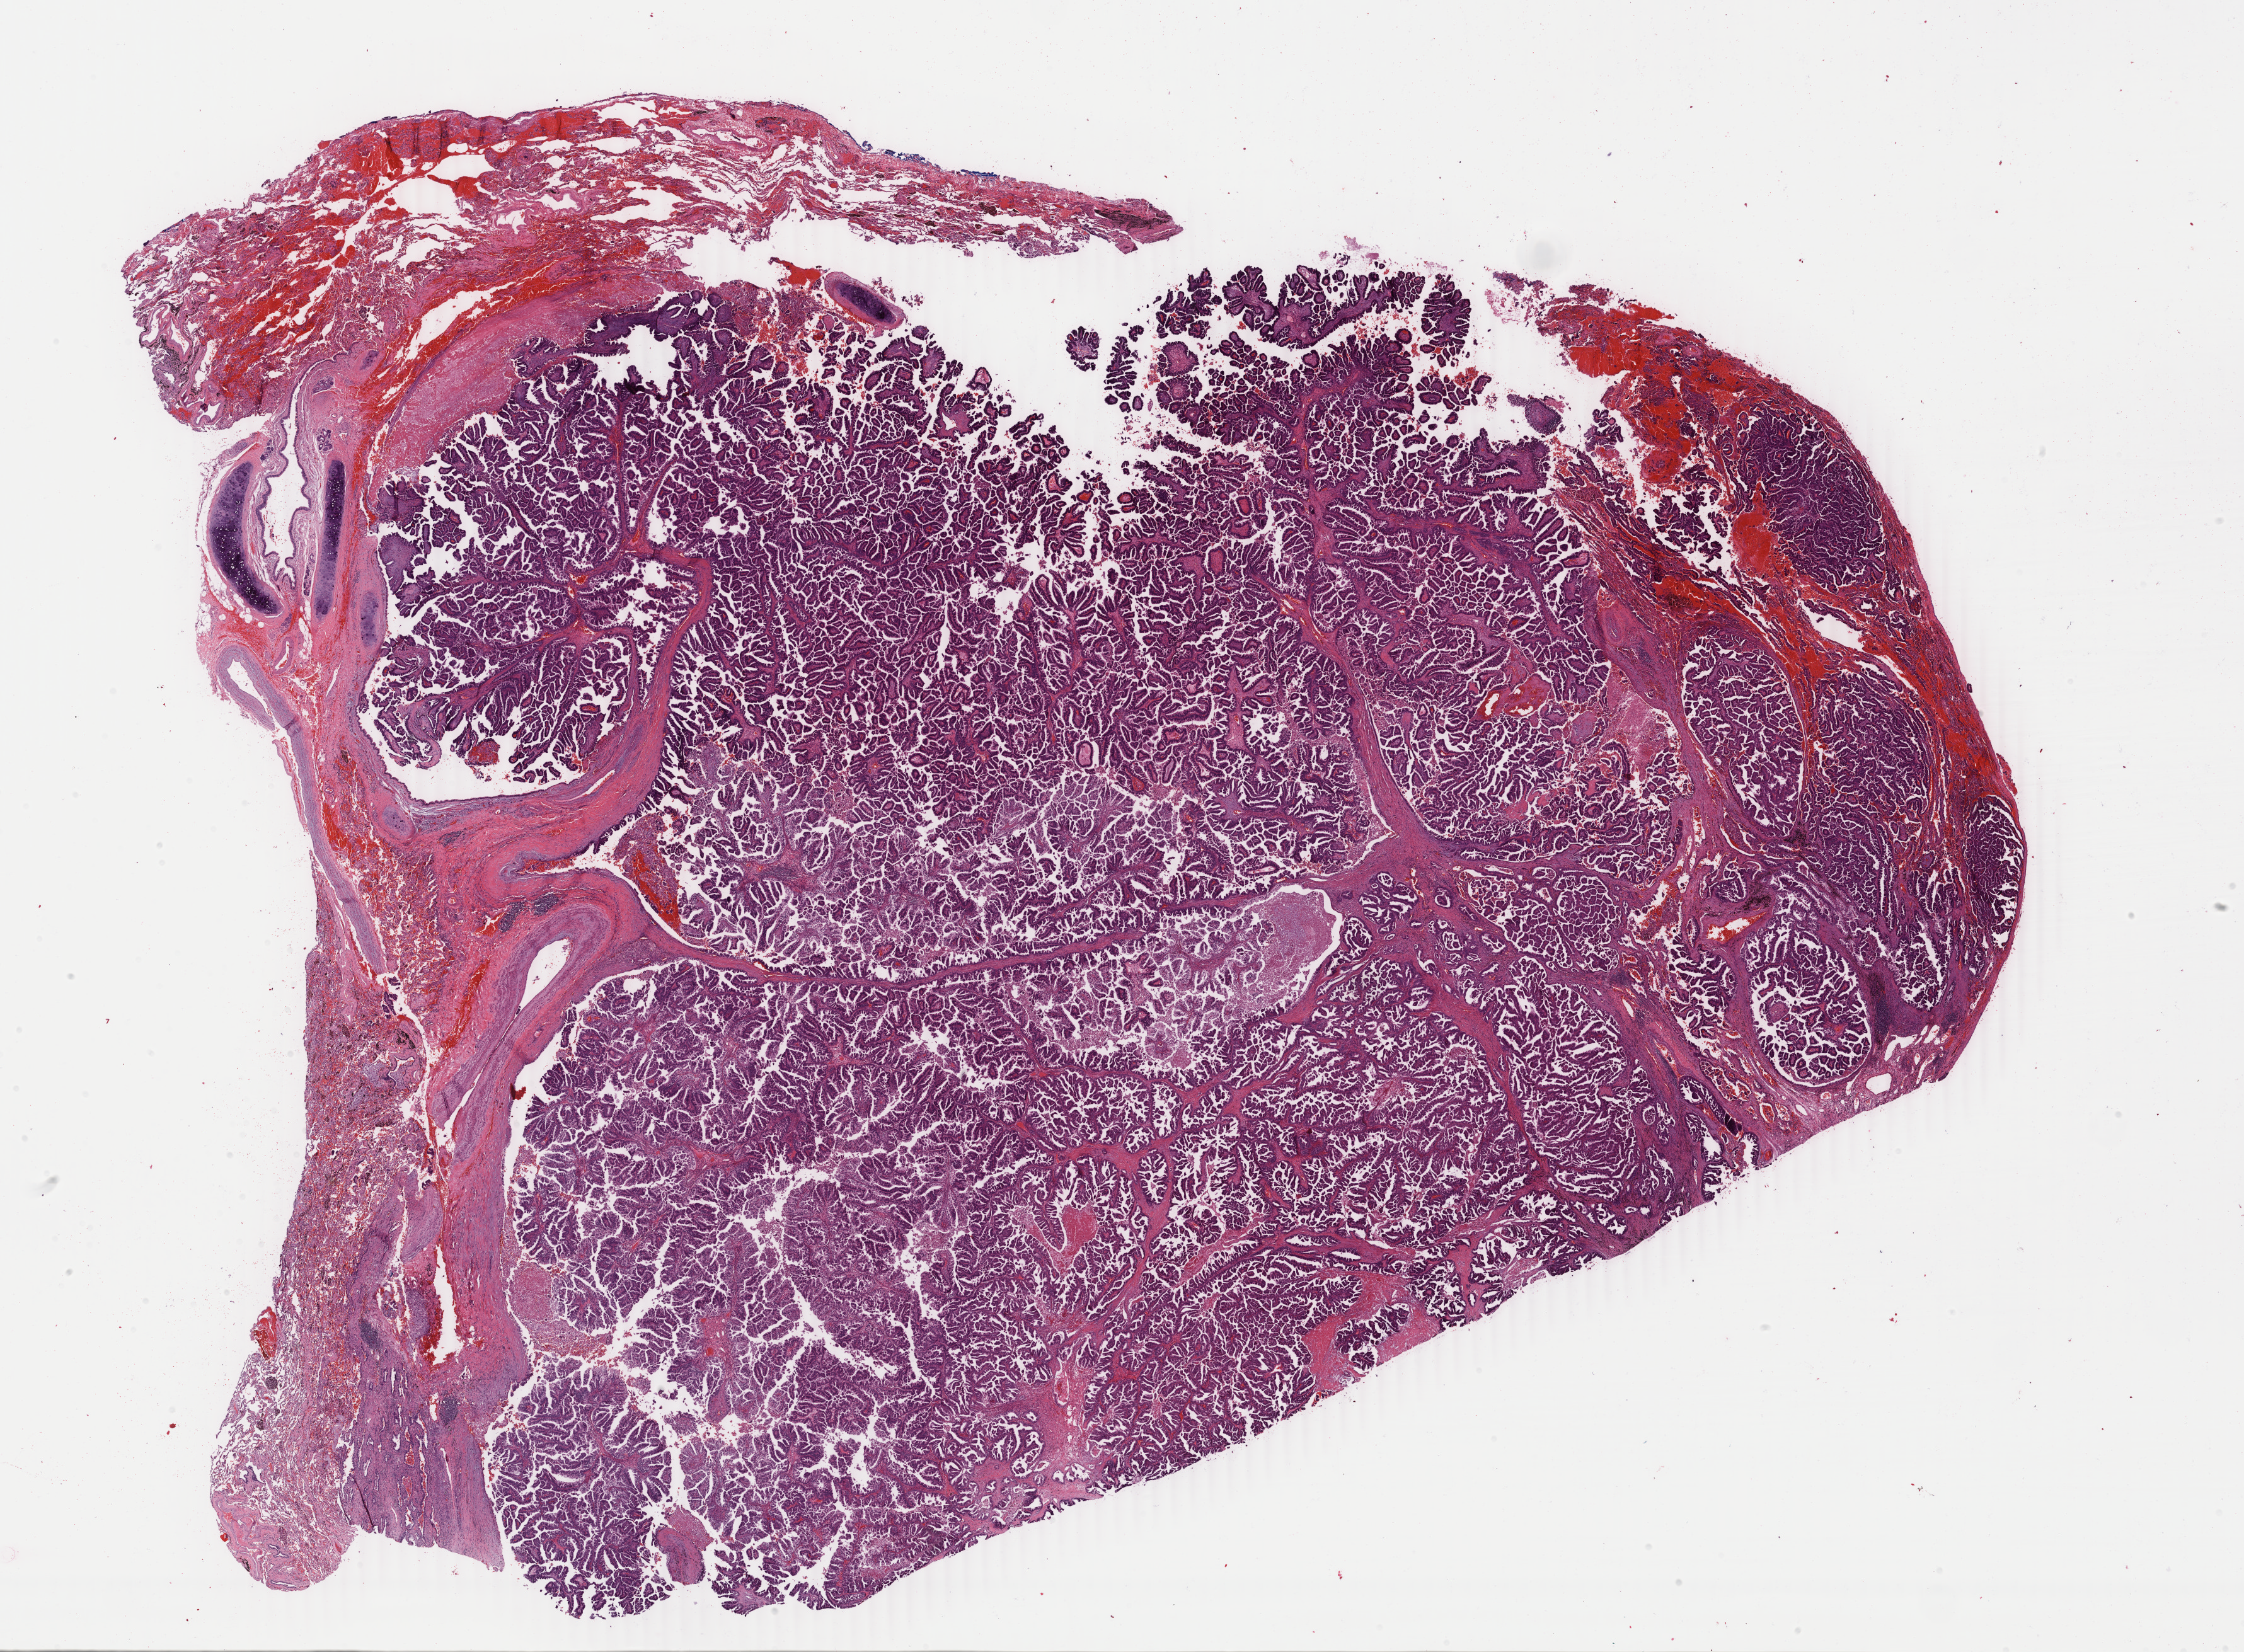
Whole-slide histology image, H&E-stained, a low-resolution overview of the entire scanned area, about 28.3 x 20.9 mm (acquisition: 40x scan); formalin-fixed paraffin-embedded (FFPE) diagnostic section; lung, primary tumour sample. Male, age 81 years at initial diagnosis.
* pathologic diagnosis: Papillary adenocarcinoma, NOS (overlapping lesion of lung)
* AJCC pathologic stage: IV (7th edition)
* TNM: T2a N2 M1a